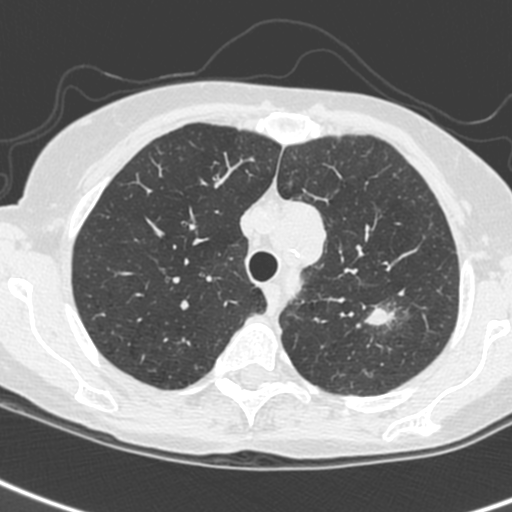
Low-dose screening chest CT, axial slice, baseline screening round, lung window (W 1500 / L -600 HU), 1.3 mm slice thickness, 120 kVp, slice 49 of 242 in the series. Female participant, aged 61 years at enrolment. Current smoker at enrolment.
- Expert-annotated lung lesion, bounding box <346,293,412,347> (left, top, right, bottom; pixels).
- The screening reader recorded 2 non-calcified nodules or masses ≥4 mm on this exam (left upper lobe, left upper lobe); which of them this box marks is not recorded.
- Lung cancer was diagnosed 29 days after this screen: small cell carcinoma, NOS, left upper lobe, stage IV (AJCC 6th edition).